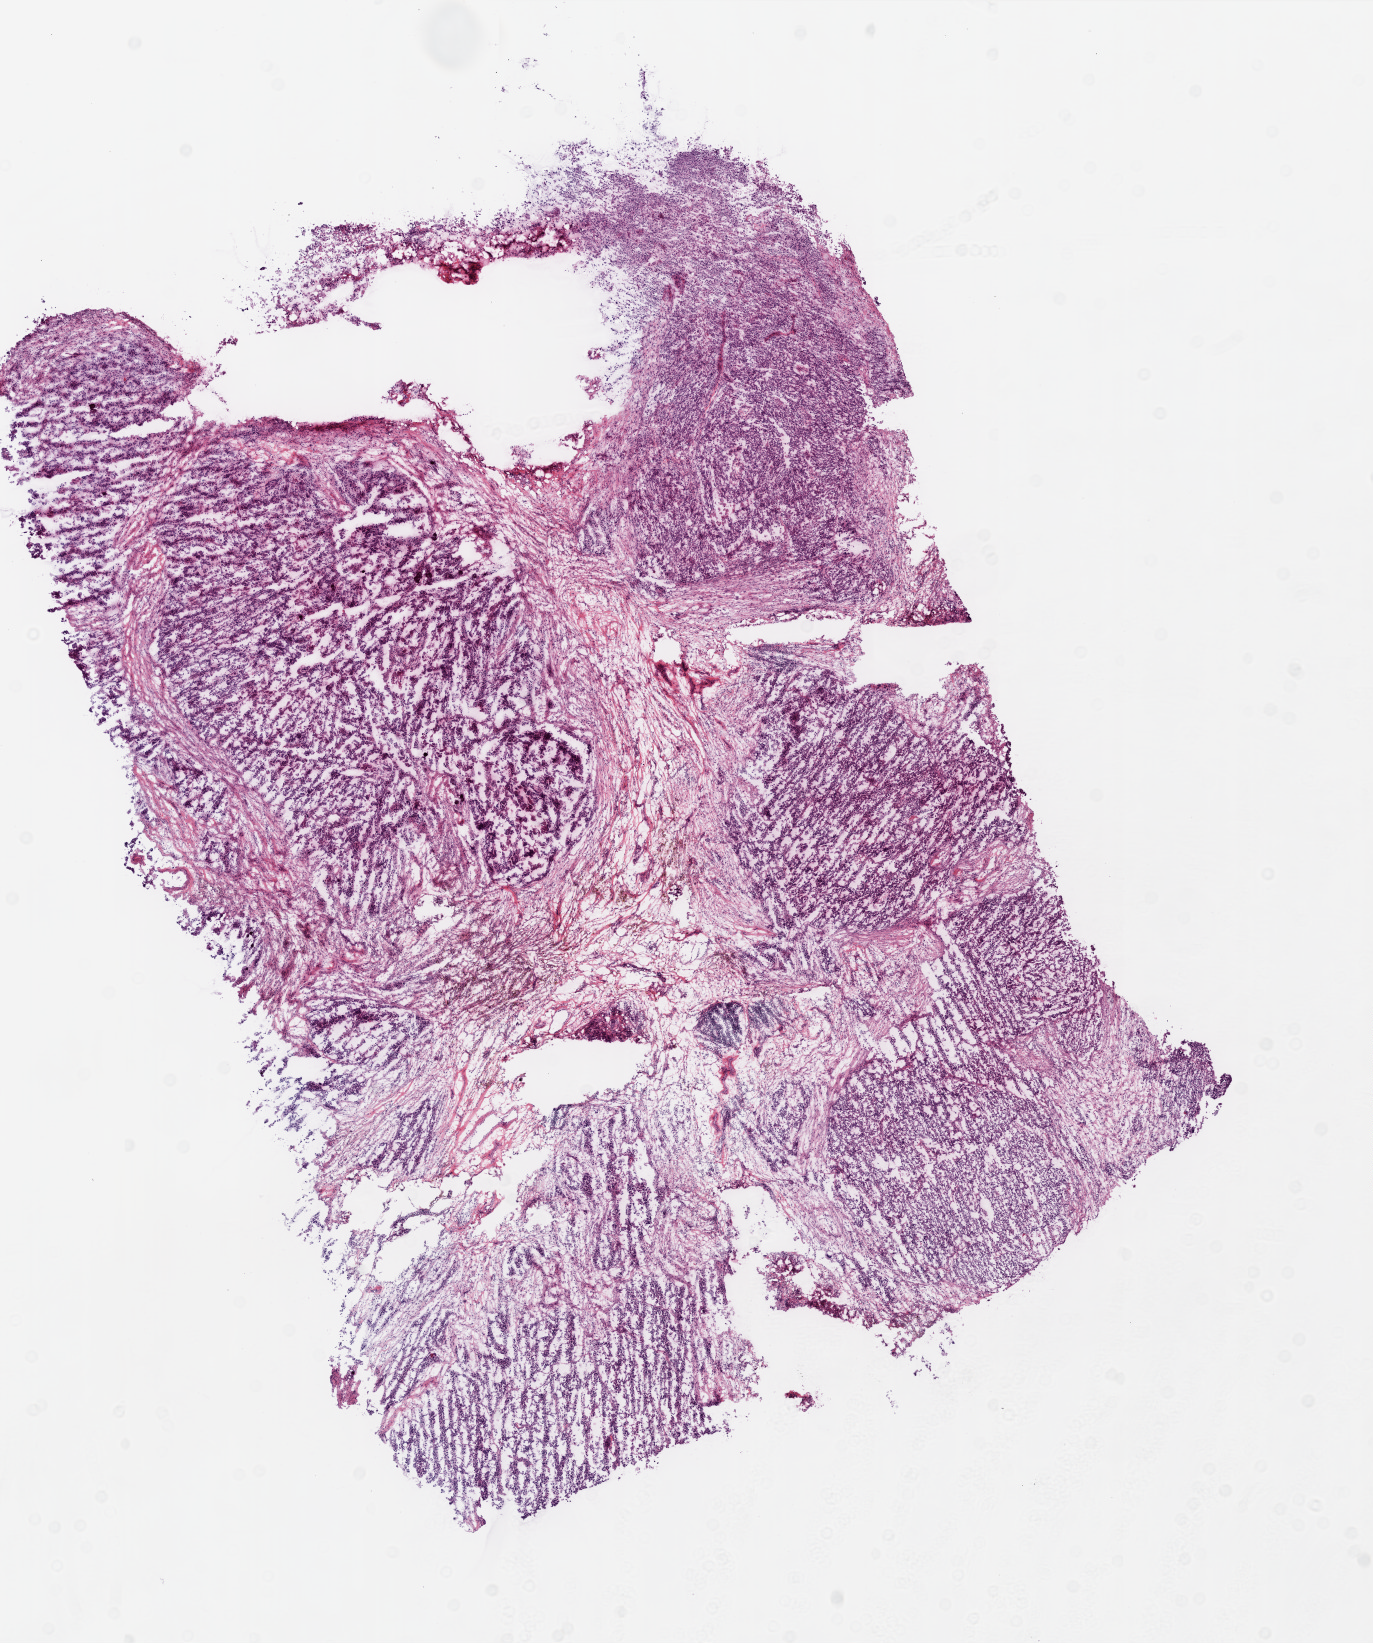
H&E-stained whole-slide image, shown as a low-resolution overview of the whole scanned area (about 11.0 x 13.1 mm, acquisition: 20x scan), frozen section from the top of the tissue portion, ovary, primary tumour sample. Female patient; age at initial diagnosis 67 years. Histologic grade: G3 (poorly differentiated). Slide review estimates, as recorded: tumour cells 65%, tumour nuclei 70%, normal cells 30%, stromal cells 0%, necrosis 5%.
* FIGO stage: IIIC
* diagnosis: Serous cystadenocarcinoma, NOS